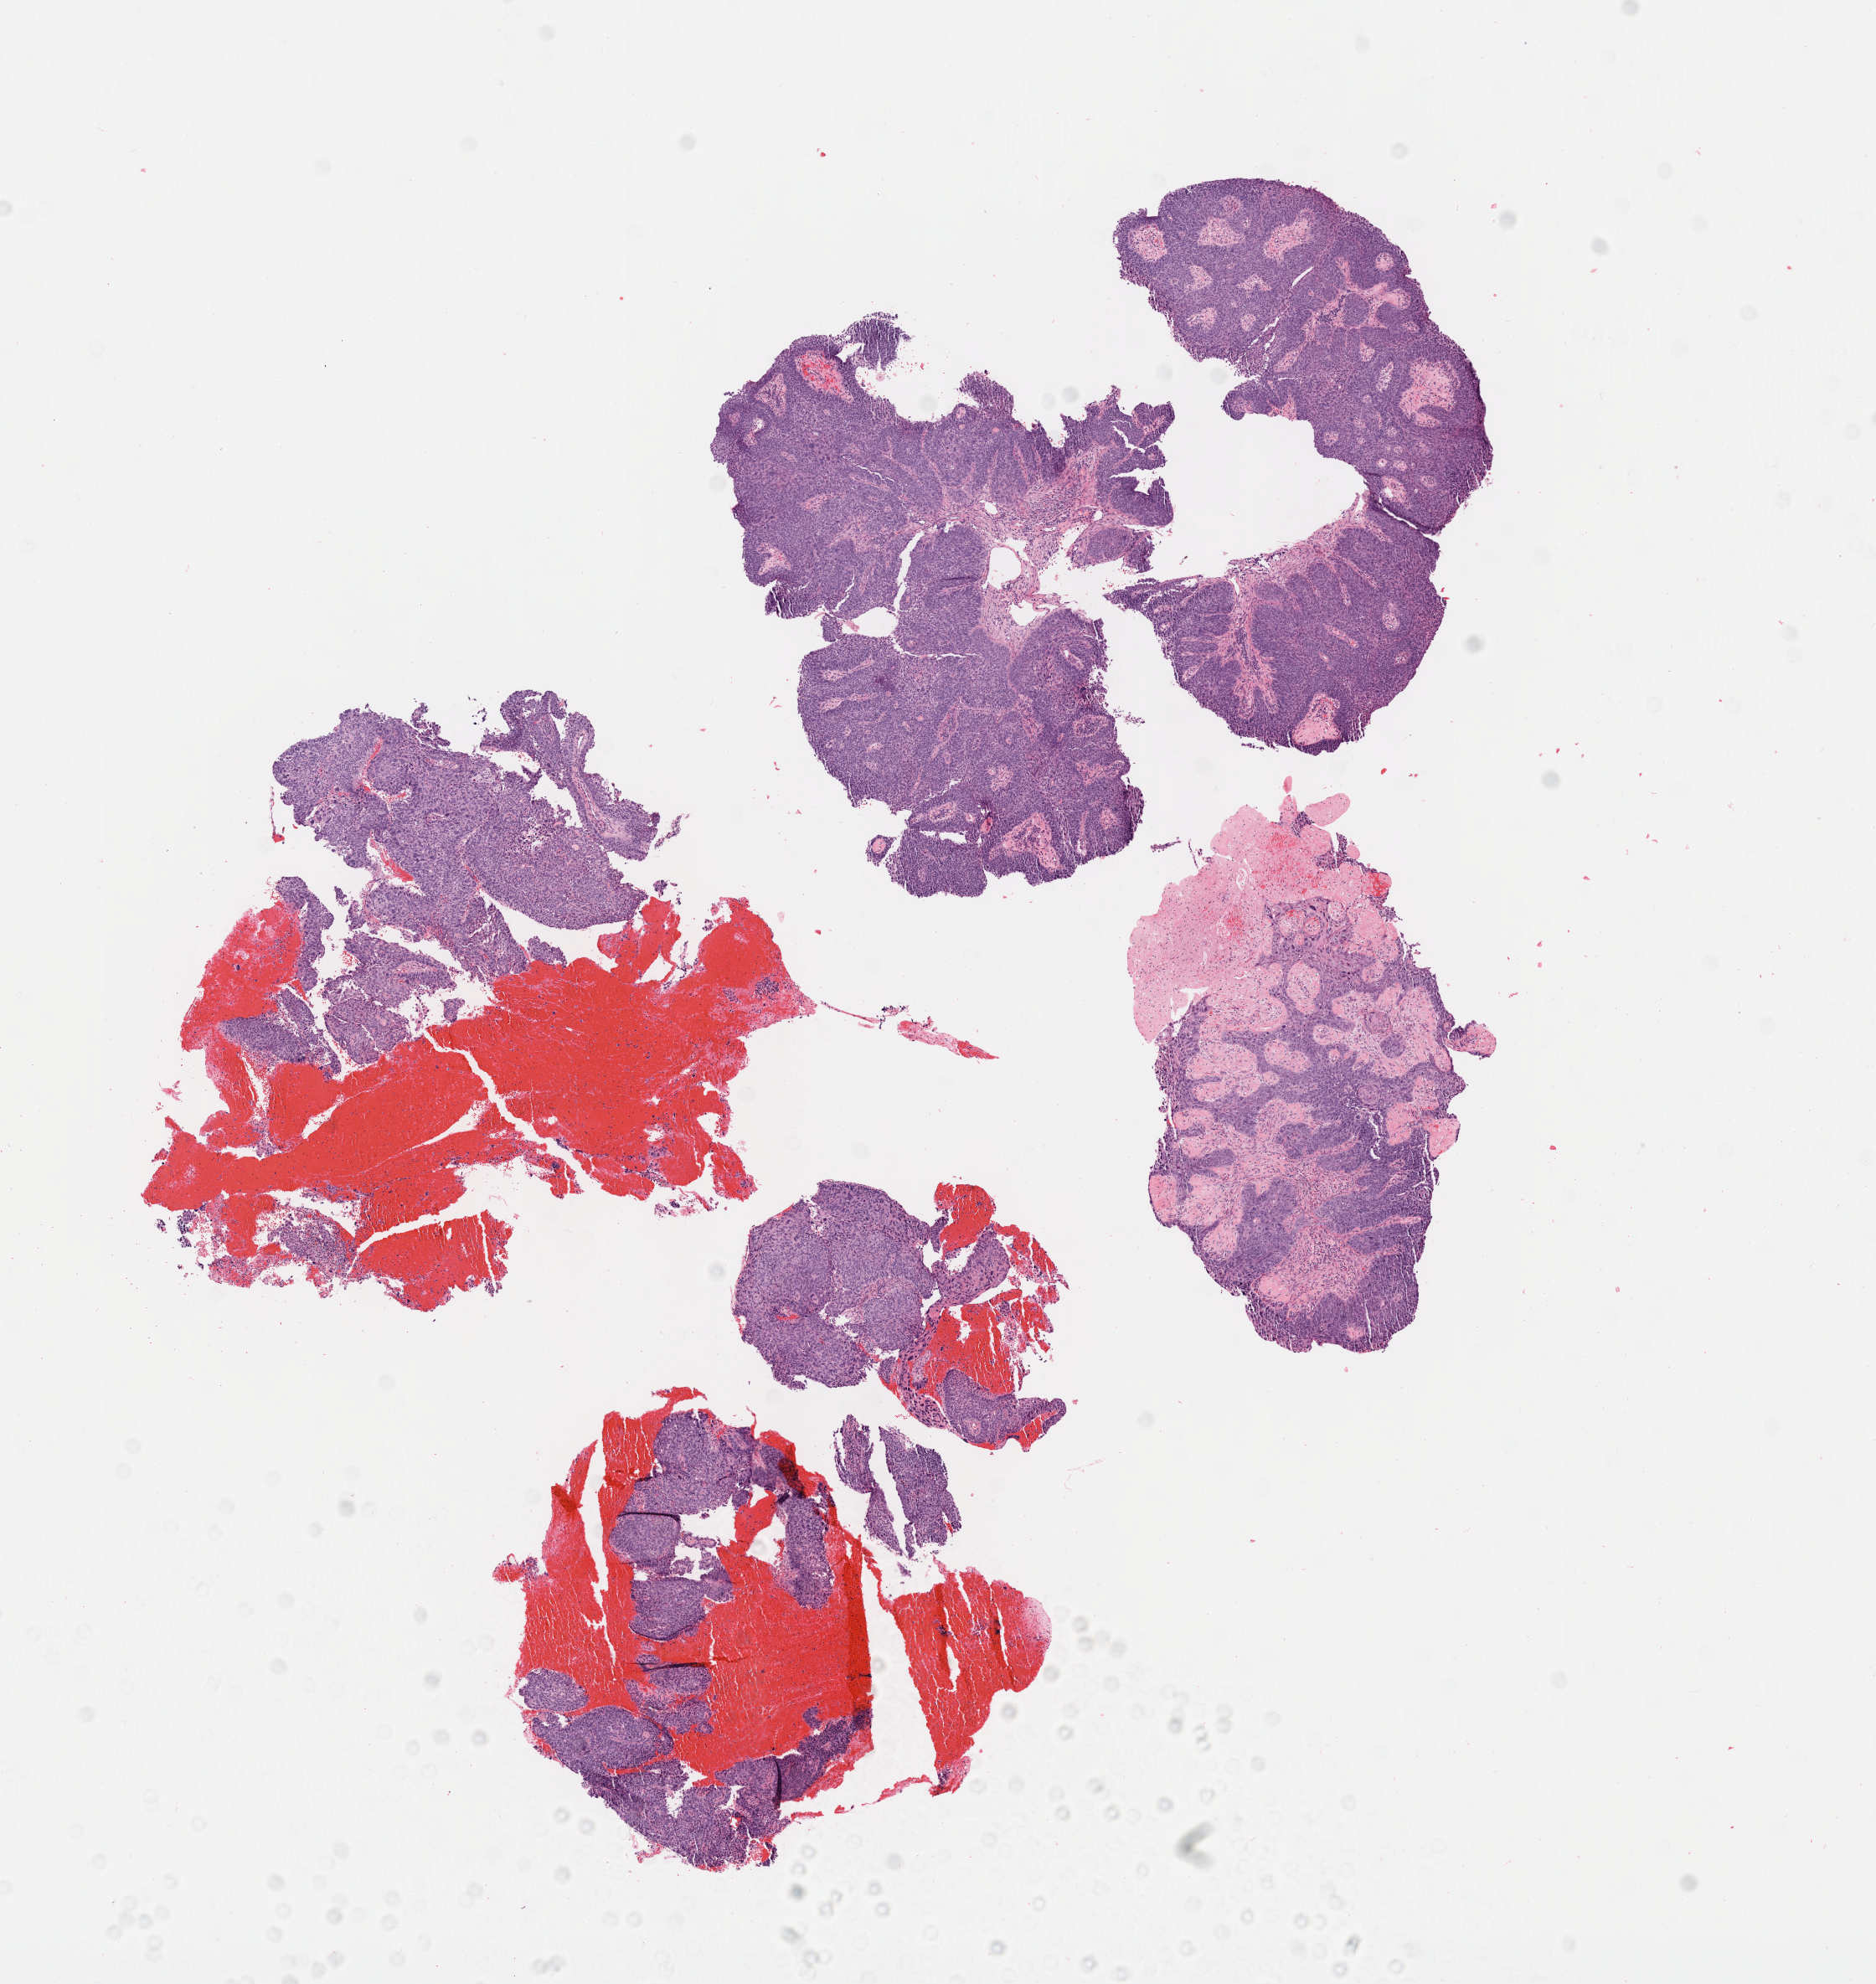
Whole-slide image, hematoxylin and eosin (H&E) stain, shown as a low-resolution overview of the whole scanned area (about 9.1 x 9.6 mm). Specimen: tumor tissue. Site: cervix. Patient female; aged 59.
Diagnosis: Squamous cell carcinoma, large cell, nonkeratinizing, NOS.